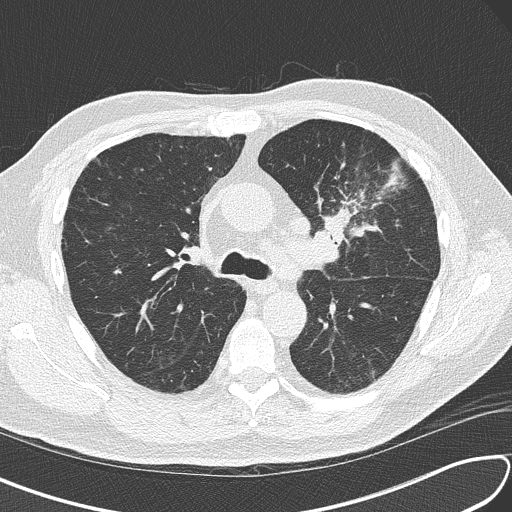
Low-dose screening chest CT, axial slice, third annual screen, lung window (W 1500 / L -600 HU), 2 mm slice thickness, lung (sharp) reconstruction kernel (B50f), slice 55 of 156 in the series, 512 × 512 image matrix, field of view 340 × 340 mm. Male, age 67 years at enrolment. Current smoker at enrolment.
Expert reader's lesion annotation, bounding box (x1, y1, x2, y2) in pixels: (298, 173, 399, 267). Reader record for this screening exam (exam-level; its link to the box is not recorded): non-calcified nodule or mass ≥4 mm, left upper lobe, 30 × 23 mm, soft tissue attenuation, pre-existing on the prior screen: no. Lung cancer was diagnosed 41 days after this screen: small cell carcinoma, NOS, left upper lobe, stage IV (AJCC 6th edition), 30 mm at pathology.